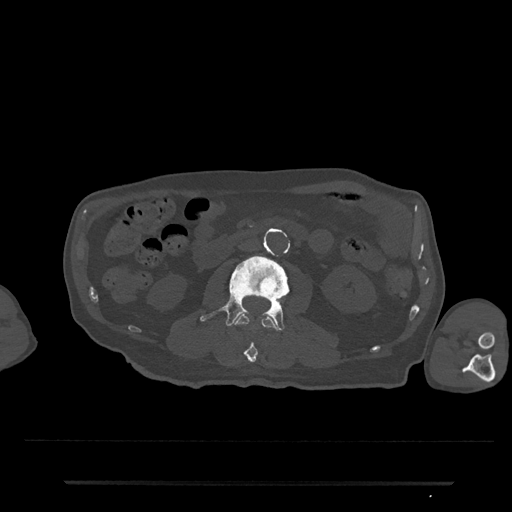
CT including the spine, one axial slice. Slice 13 of 797 in the series (ordered by position). 120 kVp. Bone window (W 1800 / L 400 HU). 512 × 512 image matrix, field of view 427 × 427 mm. Patient: male, 74 years. Case-level facts recorded for this patient, not image findings: primary cancer: prostate.
Outlined on this slice (semi-automatic segmentation, software-assisted and operator-edited):
- L2 vertebra: bounding box (x1, y1, x2, y2) in pixels: (234, 314, 279, 363)
- L3 vertebra: (200, 253, 293, 331)